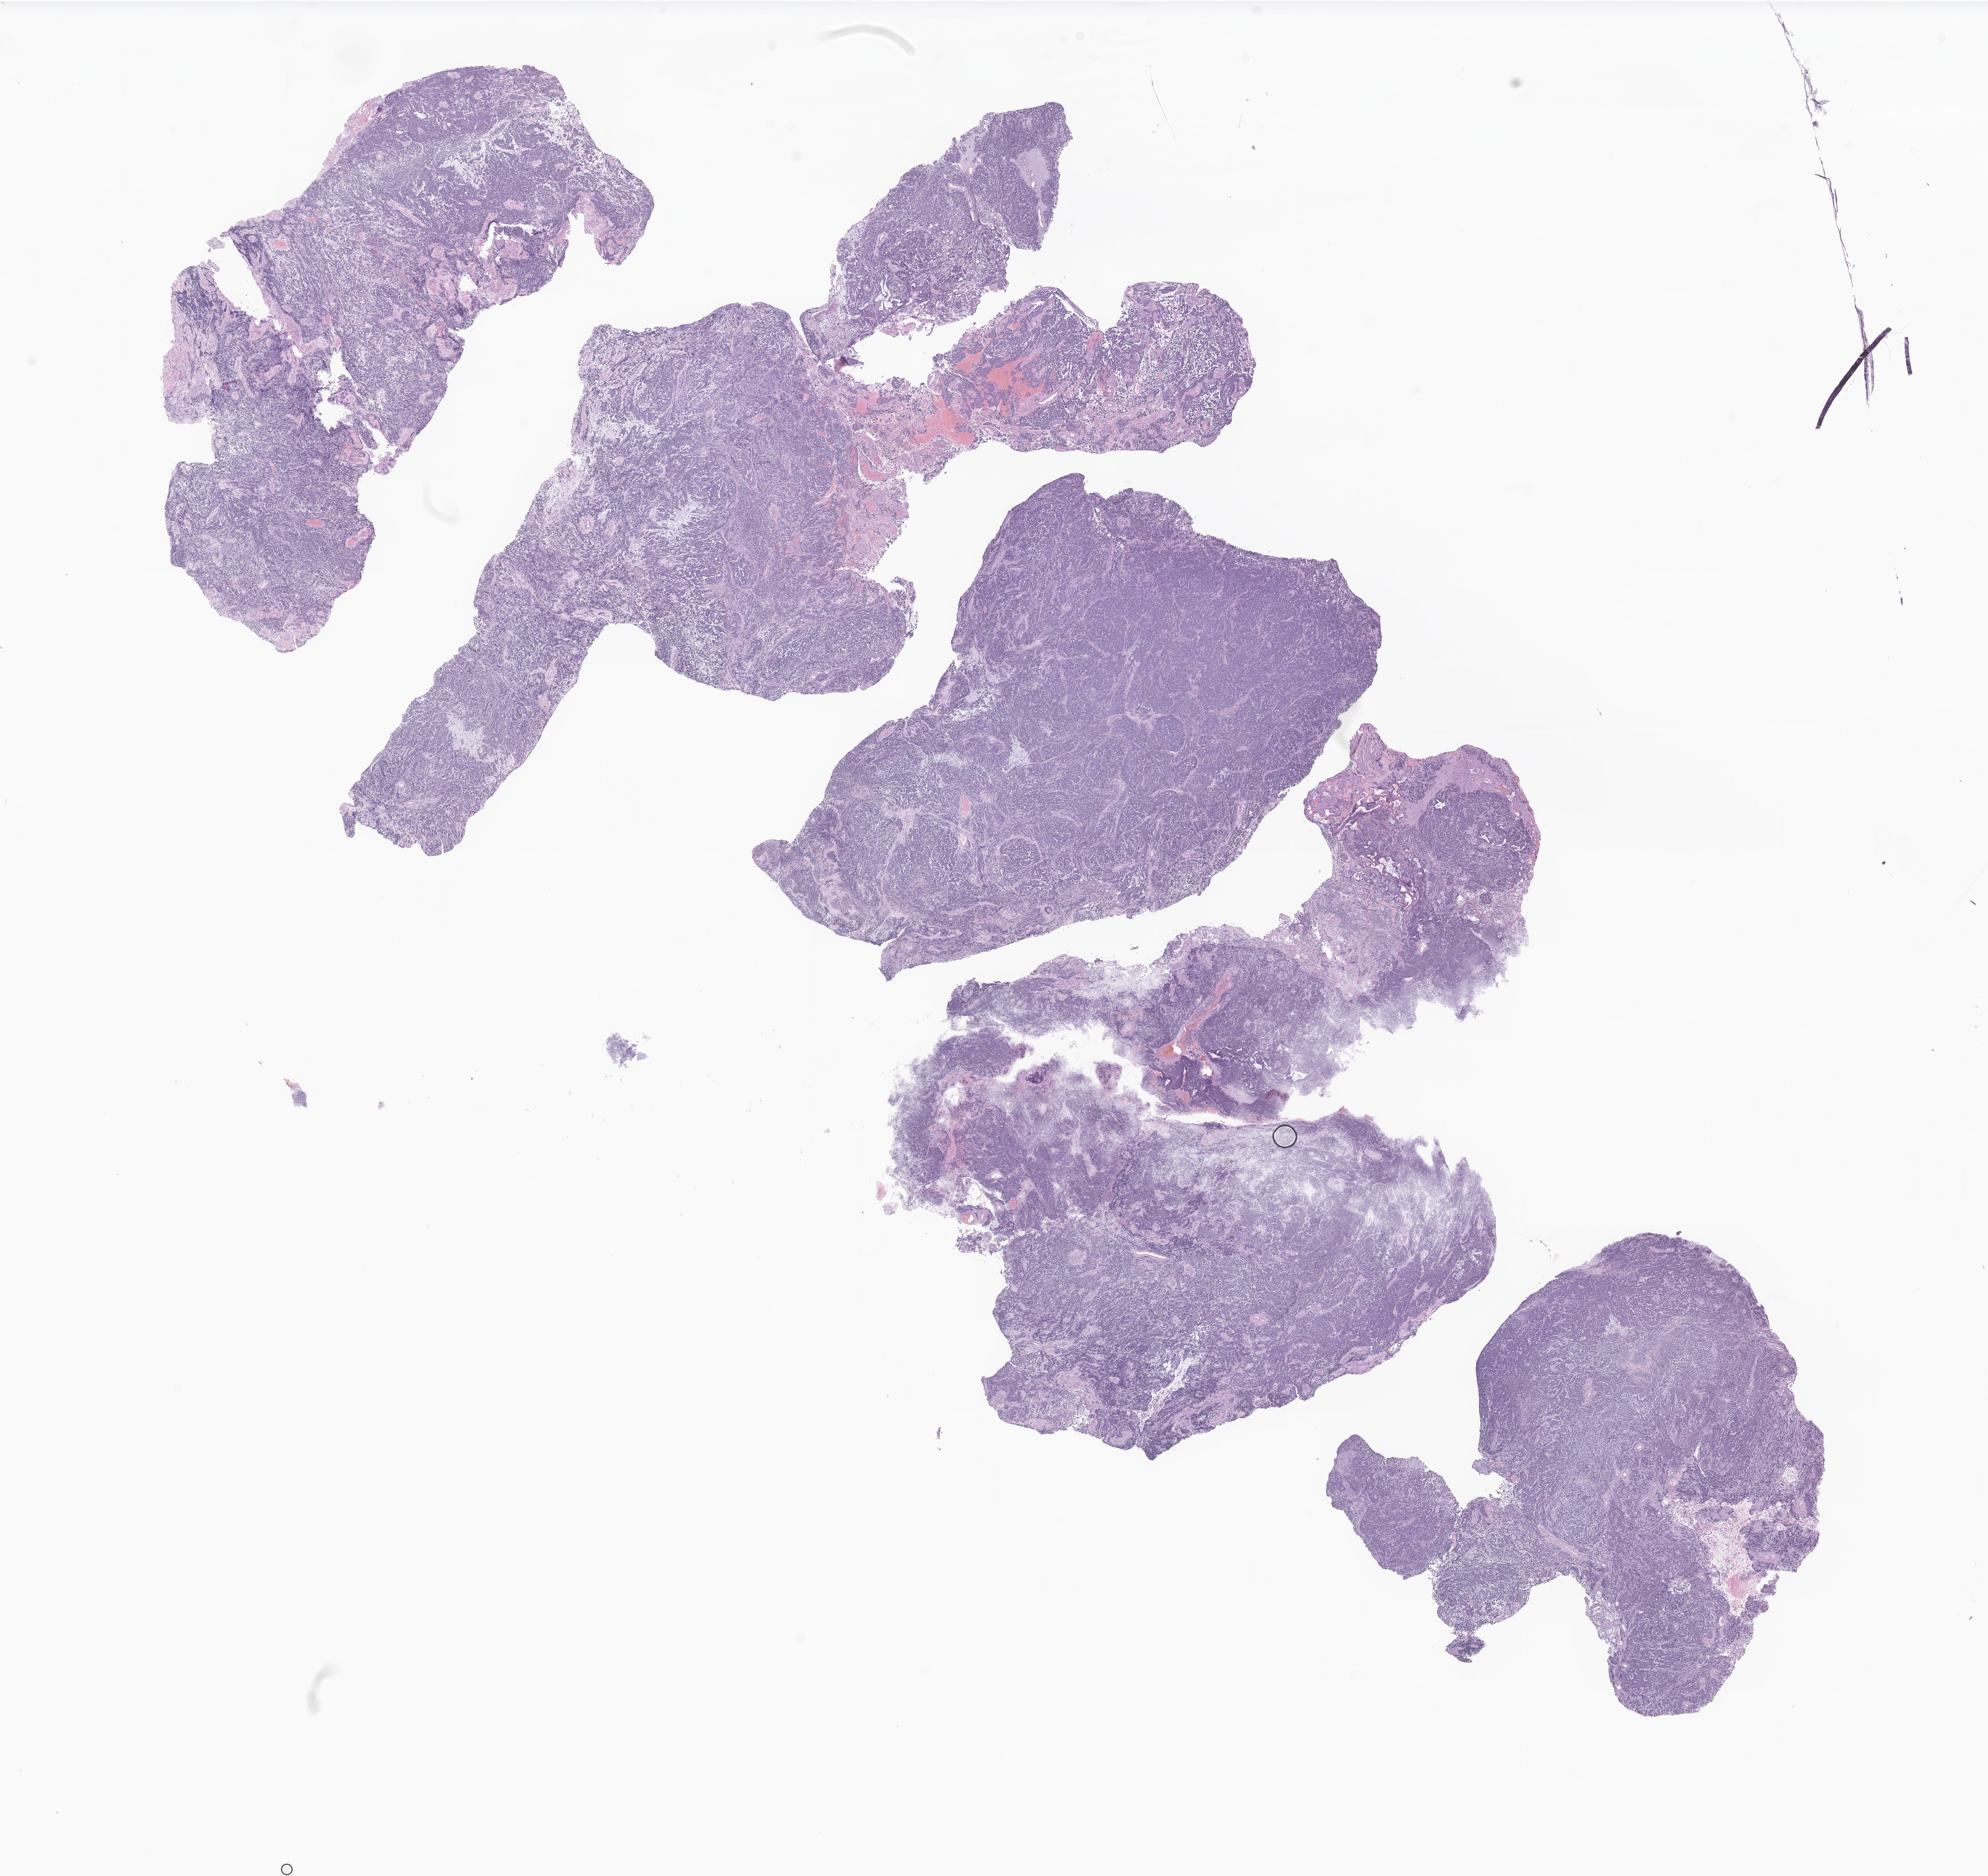
Hematoxylin and eosin (H&E) whole-slide image of tumor tissue from the brain, whole scanned area (about 22.8 x 21.5 mm) shown as a low-resolution overview; formalin-fixed paraffin-embedded section. Patient male; age 123 months (10 years 3 months).
Diagnosis (ICD-O-3 morphology term): Neoplasm, malignant.